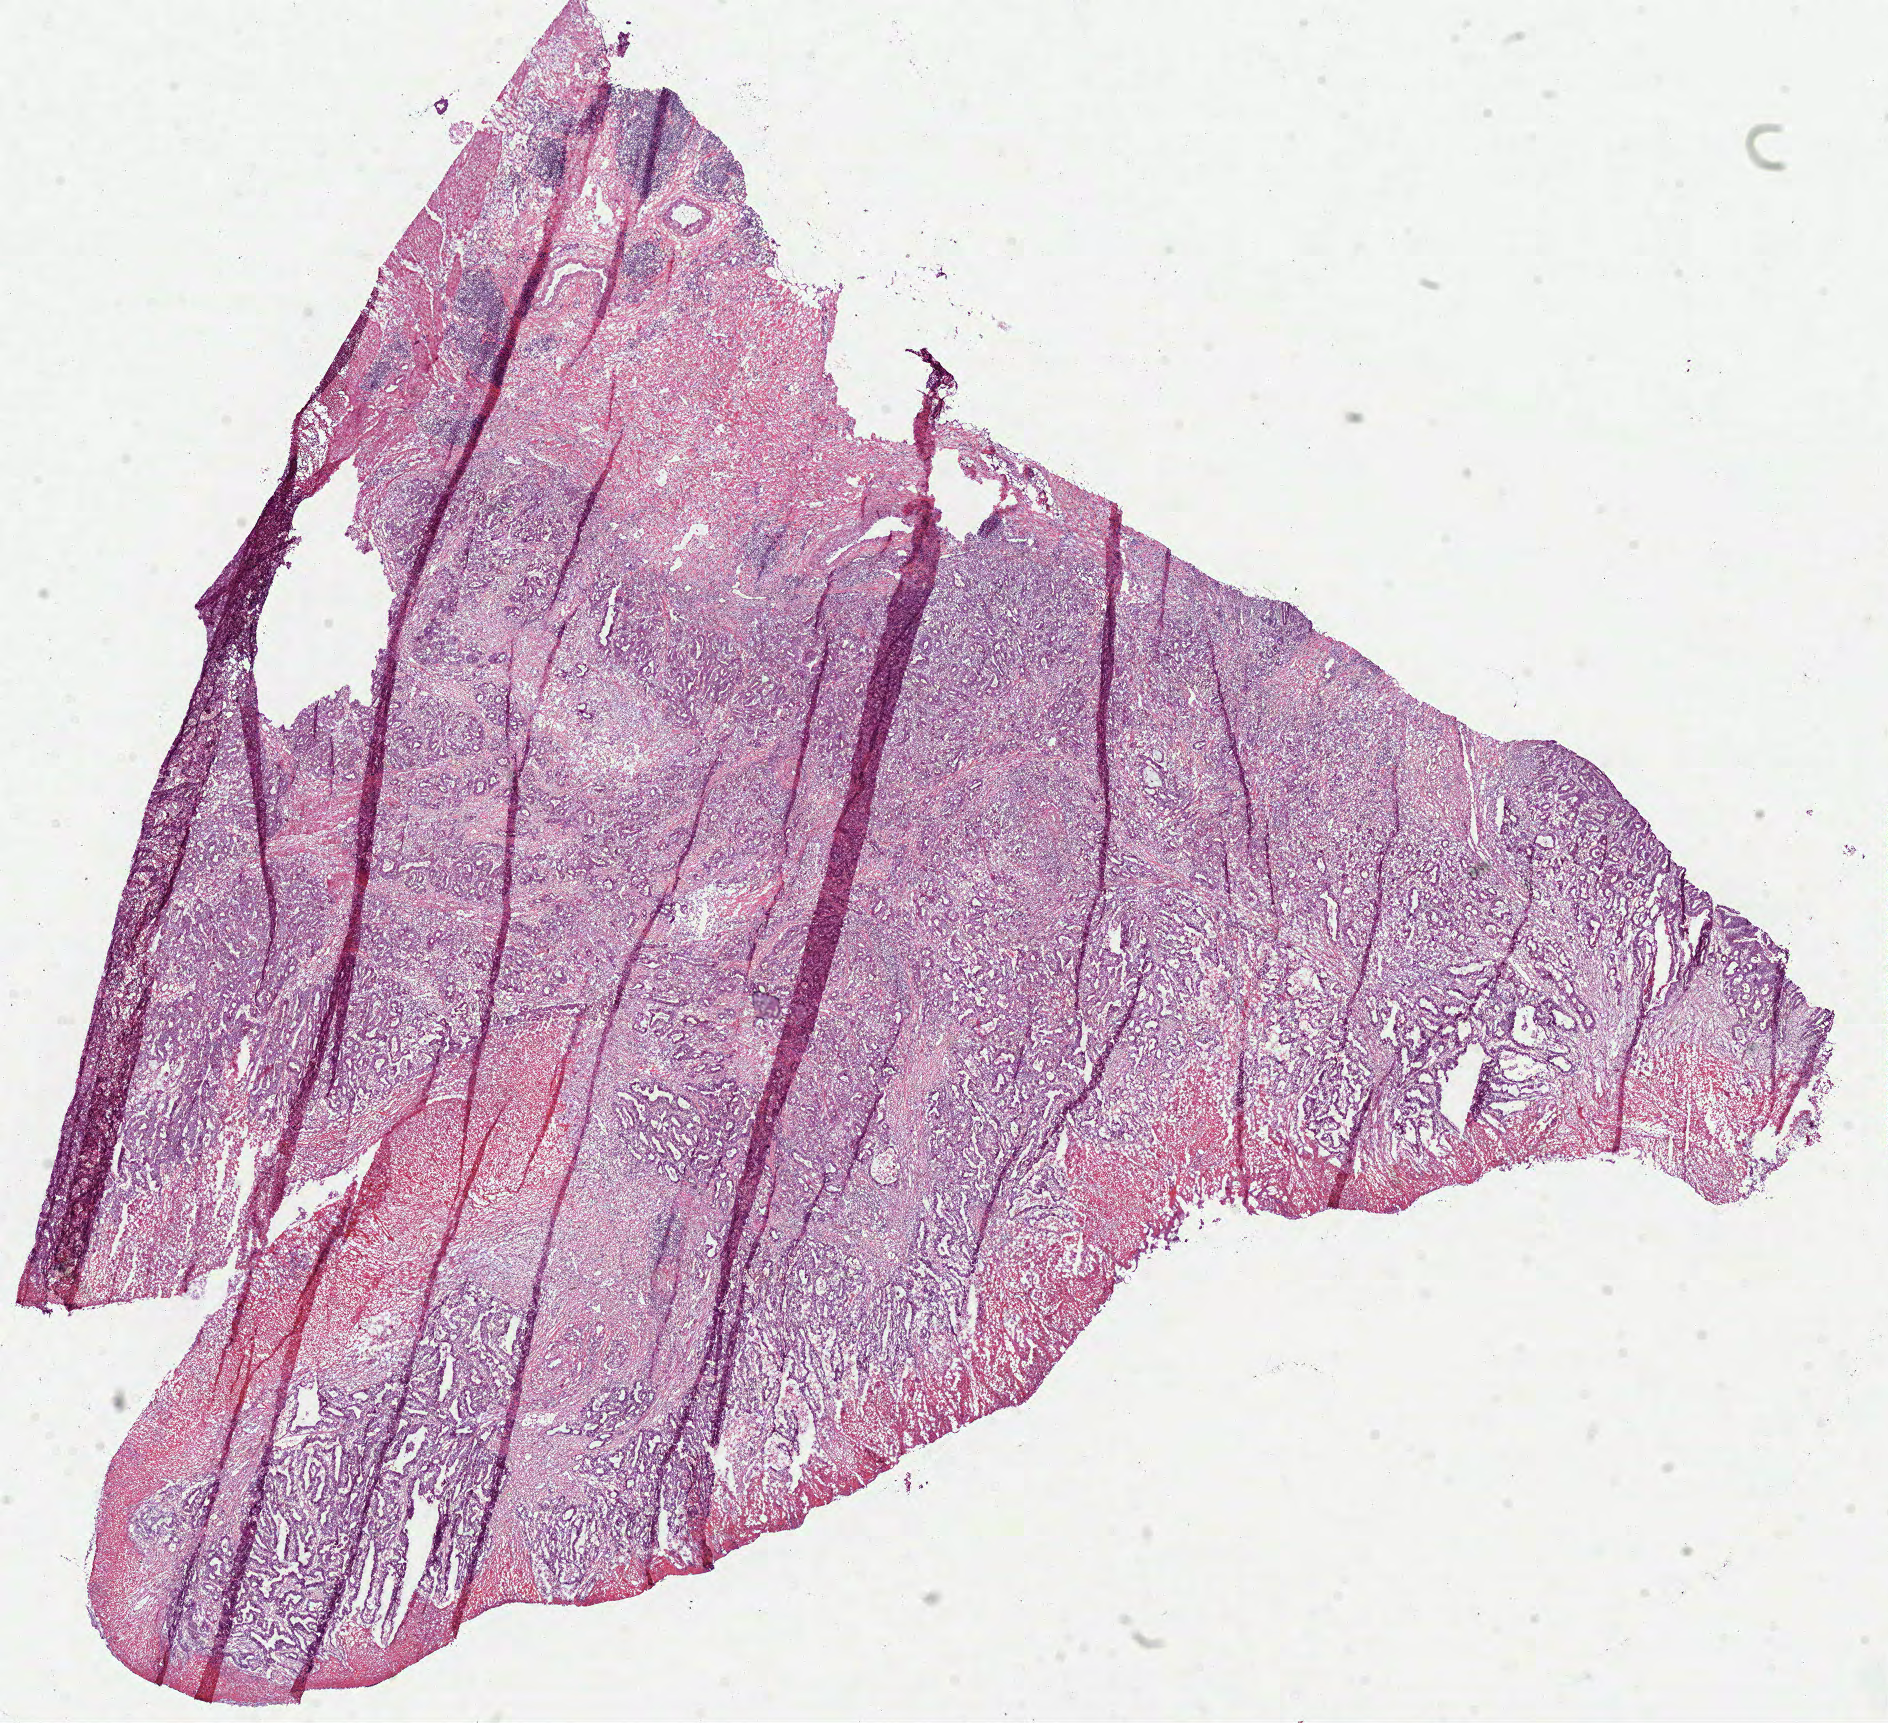
H&E-stained whole-slide image — shown as a low-resolution overview of the whole scanned area (about 15.2 x 13.9 mm, from a 40x scan); frozen section; sample: primary tumour, colon. Male patient; age at initial diagnosis 68 years. Slide review estimates, as recorded: tumour cells 75%, tumour nuclei 75%, normal cells 0%, stromal cells 20%, necrosis 5%.
AJCC pathologic stage: II. Diagnosis: Adenocarcinoma, NOS (sigmoid colon).